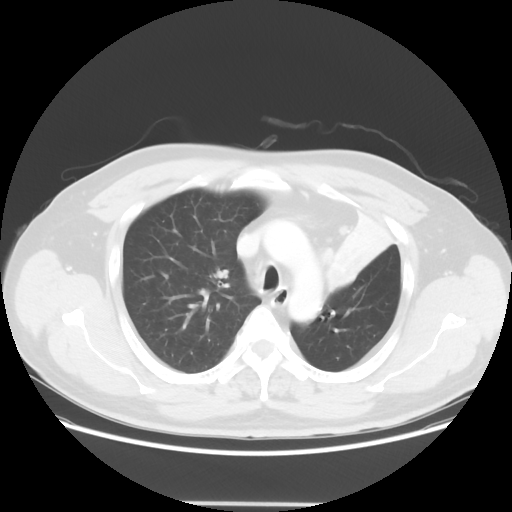
Chest CT, one axial slice. Slice 44 of 62 in the series (ordered by position). Reconstruction kernel STANDARD. 120 kVp. Lung window (W 1500 / L -600 HU). 5 mm slice thickness. 512 × 512 image matrix, field of view 403 × 403 mm. Male patient, age 49 years. From the clinical record (not read from this slice): clinical TNM (as recorded): T3 N3 M1c.
Outlined on this slice (bounding box drawn by a radiologist):
- lung tumour (recorded histology: squamous cell carcinoma): bounding box (x1, y1, x2, y2) in pixels: (316, 244, 368, 303)